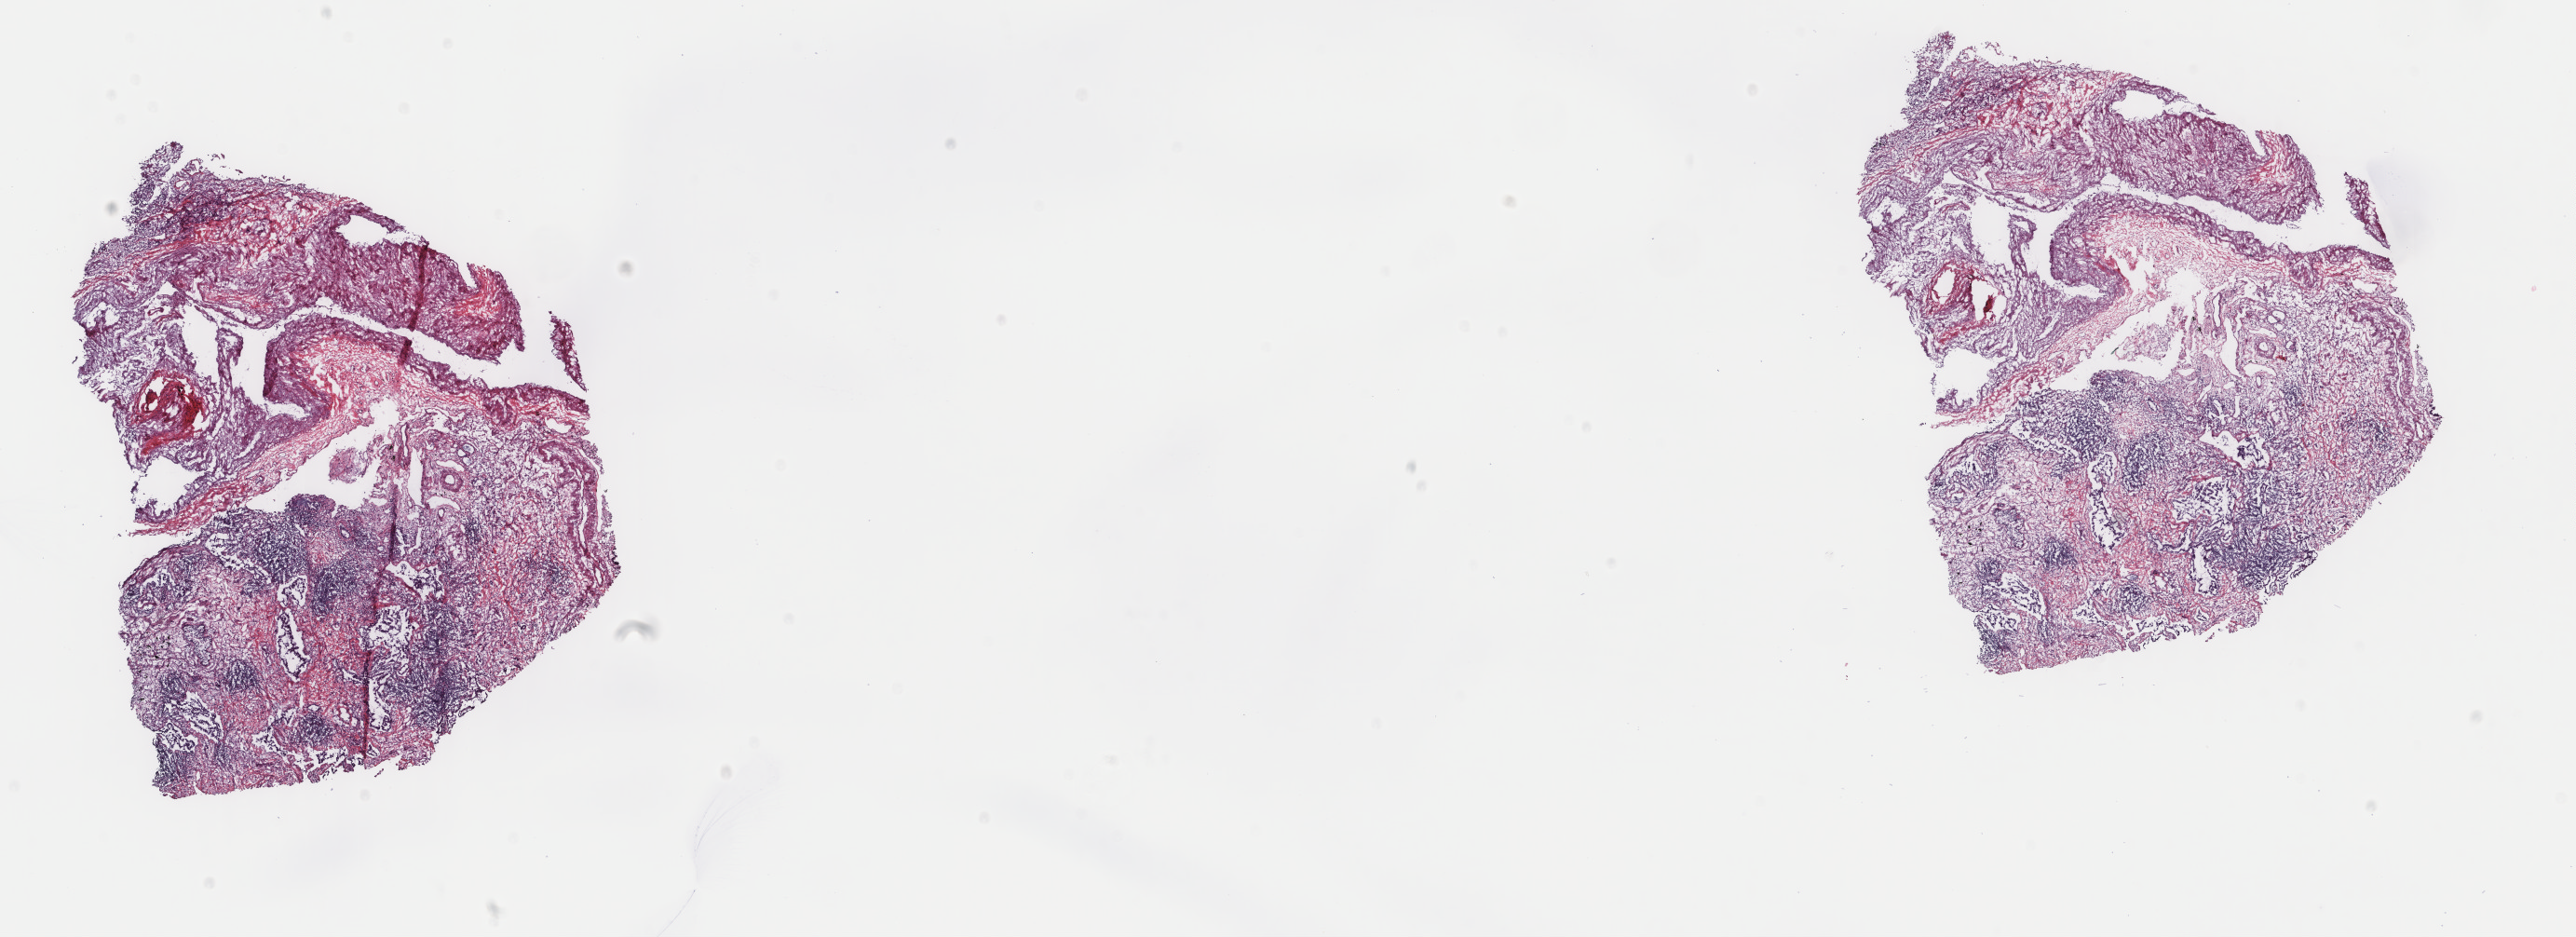
Whole-slide histology image, Hematoxylin and eosin (H&E) stained — low-resolution overview of the scanned area, about 22.0 x 8.0 mm (acquisition: 40x scan). Frozen section from the top of the tissue portion. Primary tumour sample from the lung. Female, age 76 years at initial diagnosis. Pathologist review of this section (percent, as recorded): tumour cells 60%, tumour nuclei 65%, normal cells 40%, stromal cells 0%, necrosis 0%. Inflammatory infiltration, as recorded: lymphocyte infiltration 5%, monocyte infiltration 3%, neutrophil infiltration 0%.
Histologic diagnosis: Acinar cell carcinoma (lower lobe, lung). AJCC pathologic stage: IB. Laterality: right.